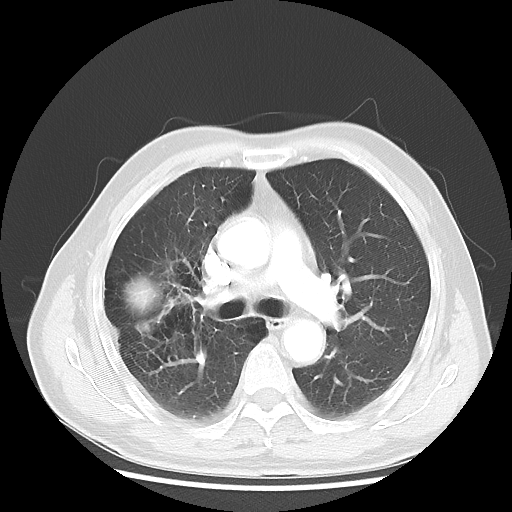
Chest CT, one axial slice. Lung window (W 1500 / L -600 HU). 5 mm slice thickness. 512 × 512 image matrix, field of view 360 × 360 mm. Patient: male, 69 years. Case-level facts recorded for this patient, not image findings: clinical TNM (as recorded): T3 N0 M0; histopathological grade: G3.
Outlined on this slice (rectangle marked by the reading radiologist):
- lung tumour (recorded histology: adenocarcinoma): box from (x=123, y=271) to (x=165, y=334) px